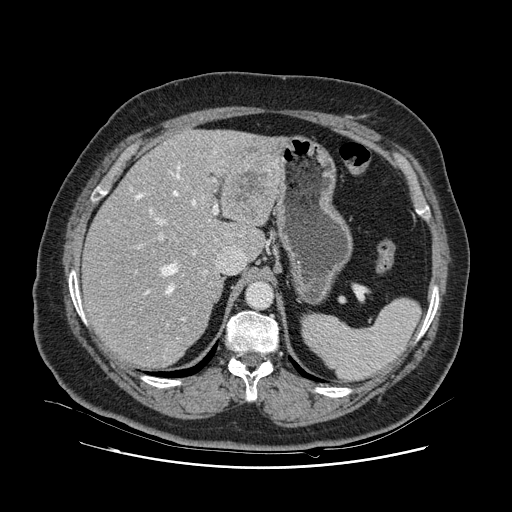
Contrast-enhanced abdominal CT, one axial slice; position 79 of 132 along the scan axis; intravenous contrast given; soft-tissue window (W 400 / L 40 HU); 2.5 mm slice thickness; 512 × 512 image matrix. Female patient, age 73 years. Case-level facts recorded for this patient, not image findings: diagnosis: colorectal cancer liver metastases, imaged before liver resection; multiple liver metastases: no; largest metastasis: 7 cm; disease in both lobes: no.
Outlined on this slice (manually delineated by an expert):
- hepatic veins: bounding box <135,151,243,358> (left, top, right, bottom; pixels)
- liver: <83,131,278,366>
- planned liver remnant (the part of the liver to remain after resection): <83,159,238,367>
- portal vein (with intrahepatic branches): <137,178,218,326>
- liver metastasis: <234,165,268,217>